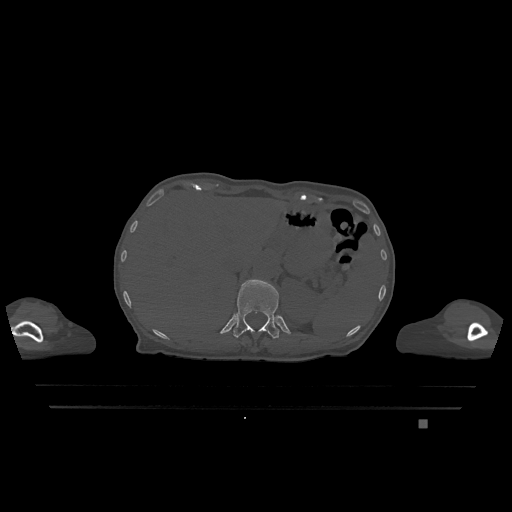
CT including the spine, one axial slice; position 537 of 1317 along the scan axis; bone window (W 1800 / L 400 HU); 512 × 512 image matrix, field of view 500 × 500 mm. Patient: female, 74 years. Case-level facts recorded for this patient, not image findings: primary cancer: lung; vertebrae with lytic lesions (as recorded): T1, T4, T5, T6, L4, L5.
Structures marked on this image (semi-automatically segmented with operator editing):
- T12 vertebra: box from (x=233, y=279) to (x=279, y=339) px